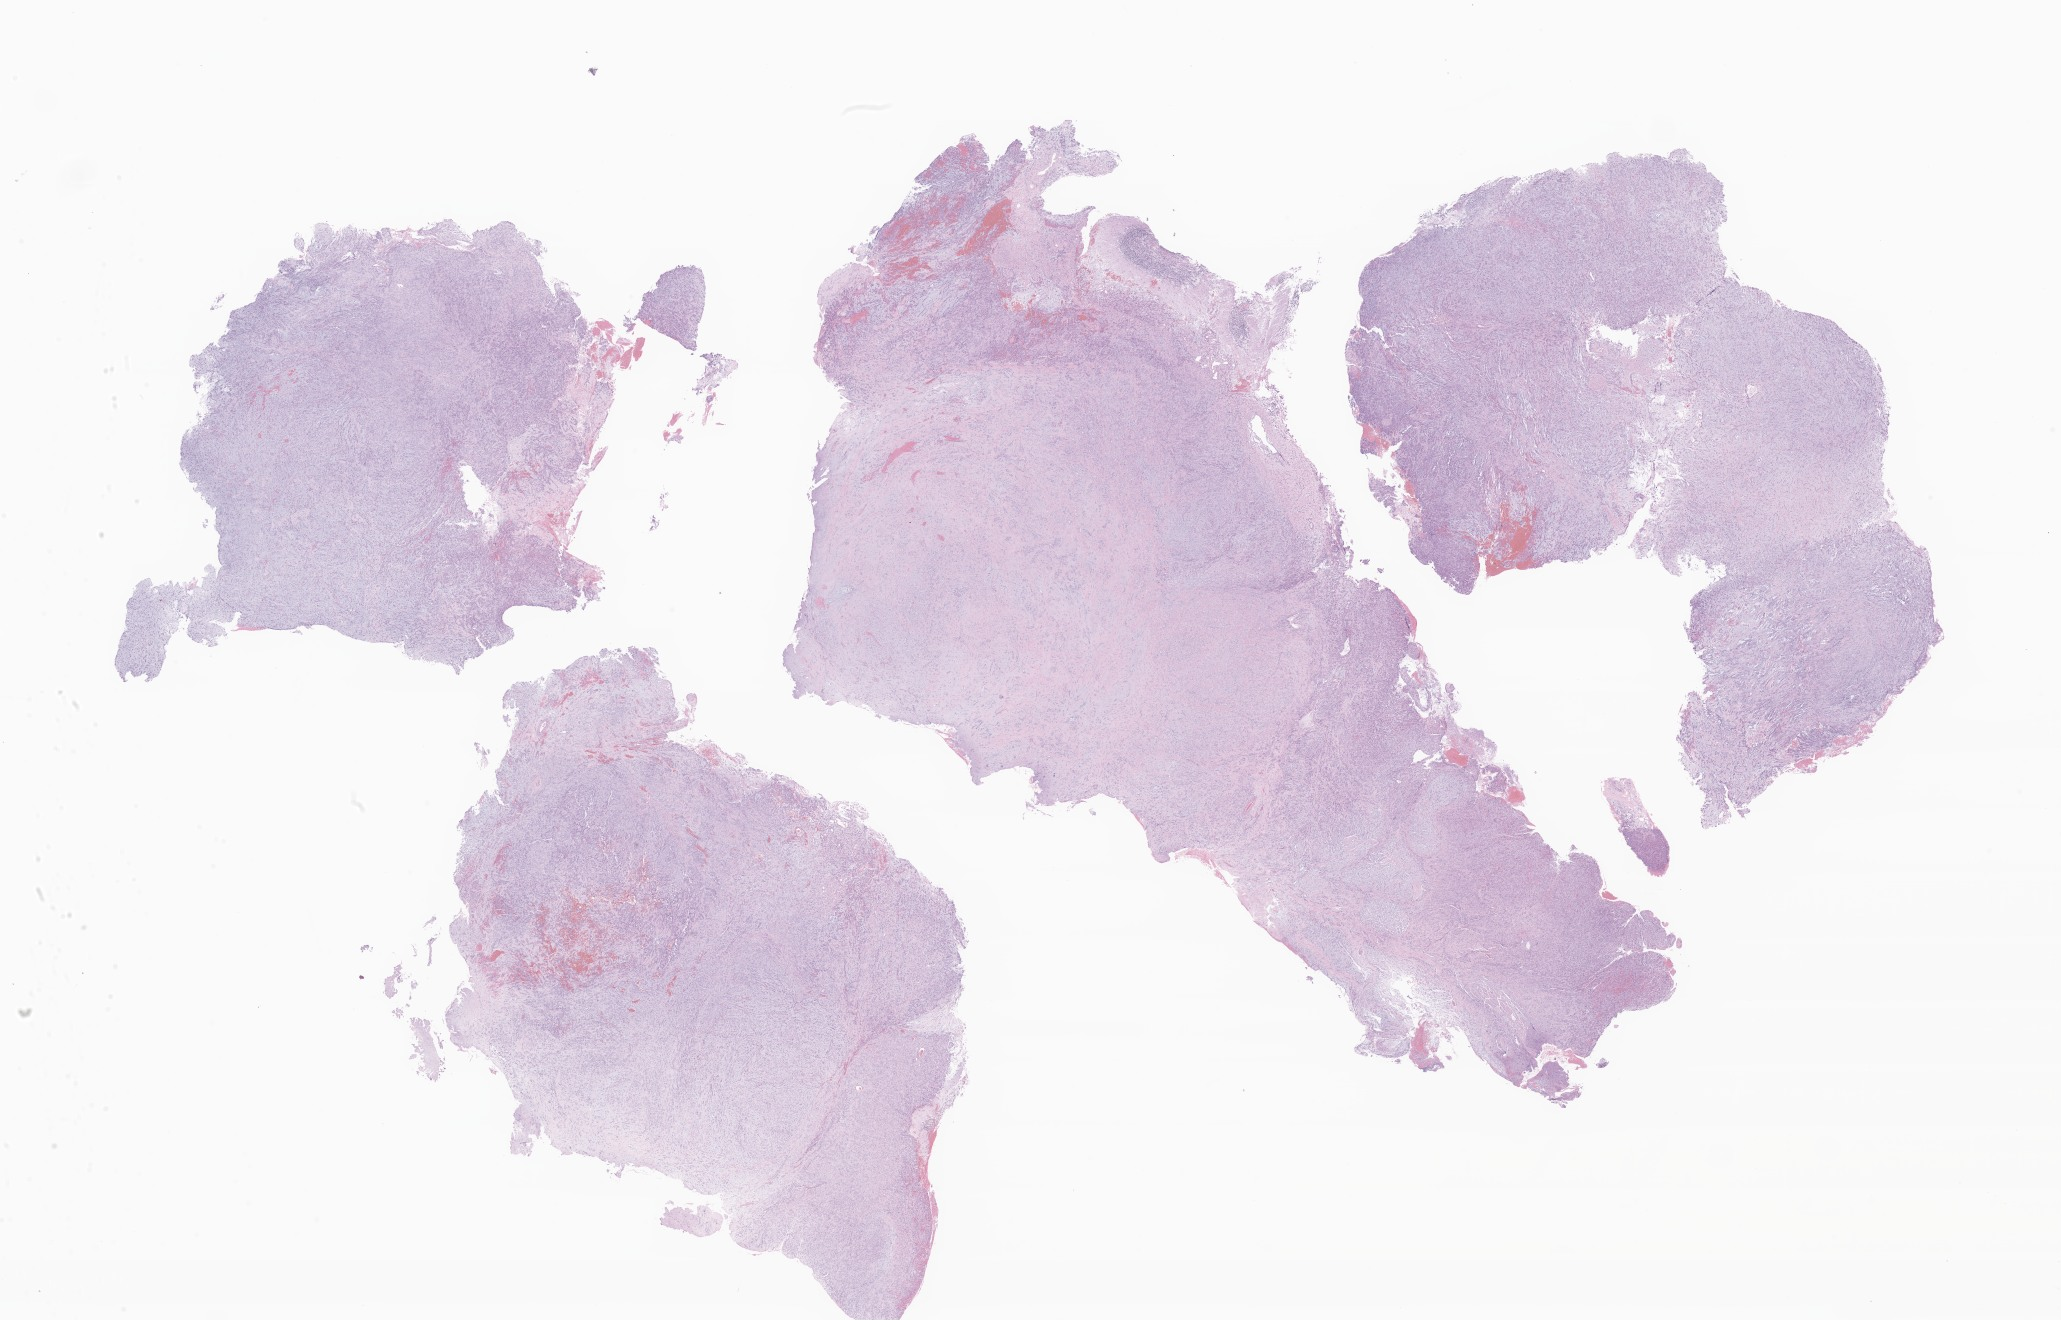
Whole-slide image, hematoxylin and eosin (H&E) stain of tumor tissue from the brain stem — a low-resolution overview of the entire scanned area, about 34.8 x 22.3 mm. FFPE section. Patient: male, age 80 months (6 years 8 months).
Diagnosis: Atypical teratoid/rhabdoid tumor.